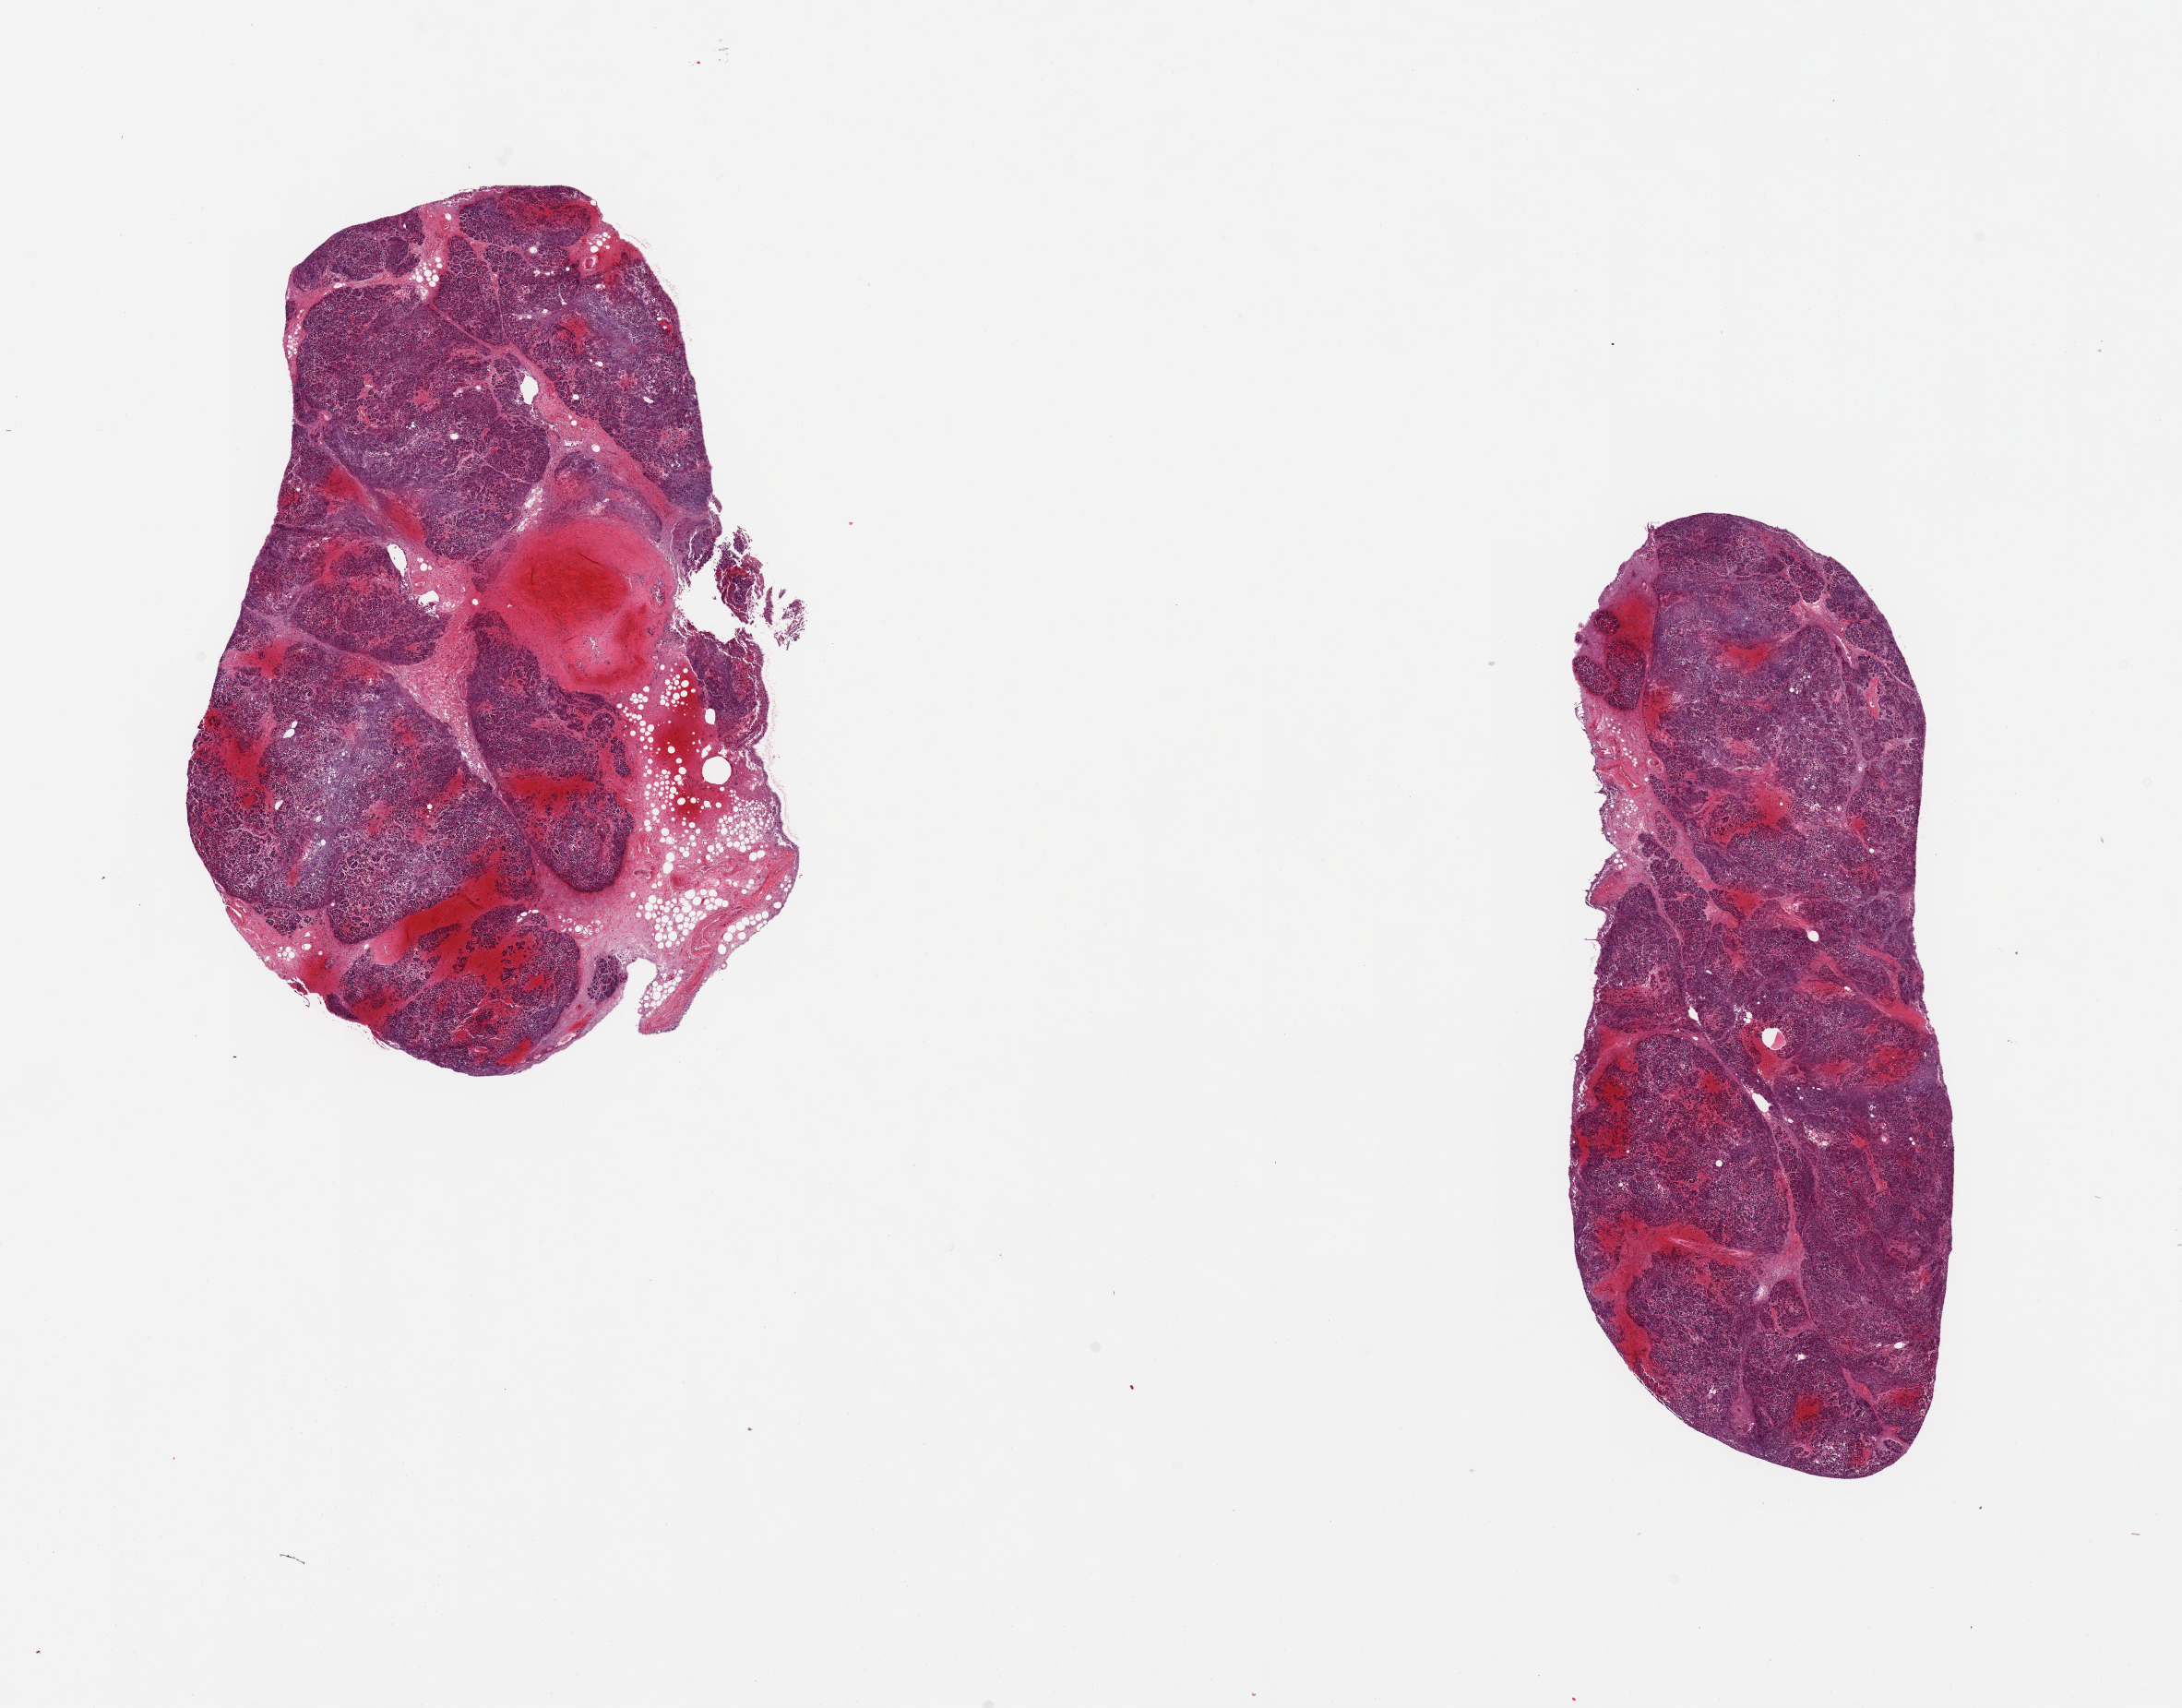
Haematoxylin and eosin whole-slide image, brightfield, shown as a low-resolution overview of the whole scanned area (about 18.7 x 14.6 mm, acquisition: 20x scan). PAXgene-fixed paraffin-embedded (PFPE) section. Sampled site (target tissue): pancreas. Tissue donor sample.
Review note (as recorded): 2 pieces.